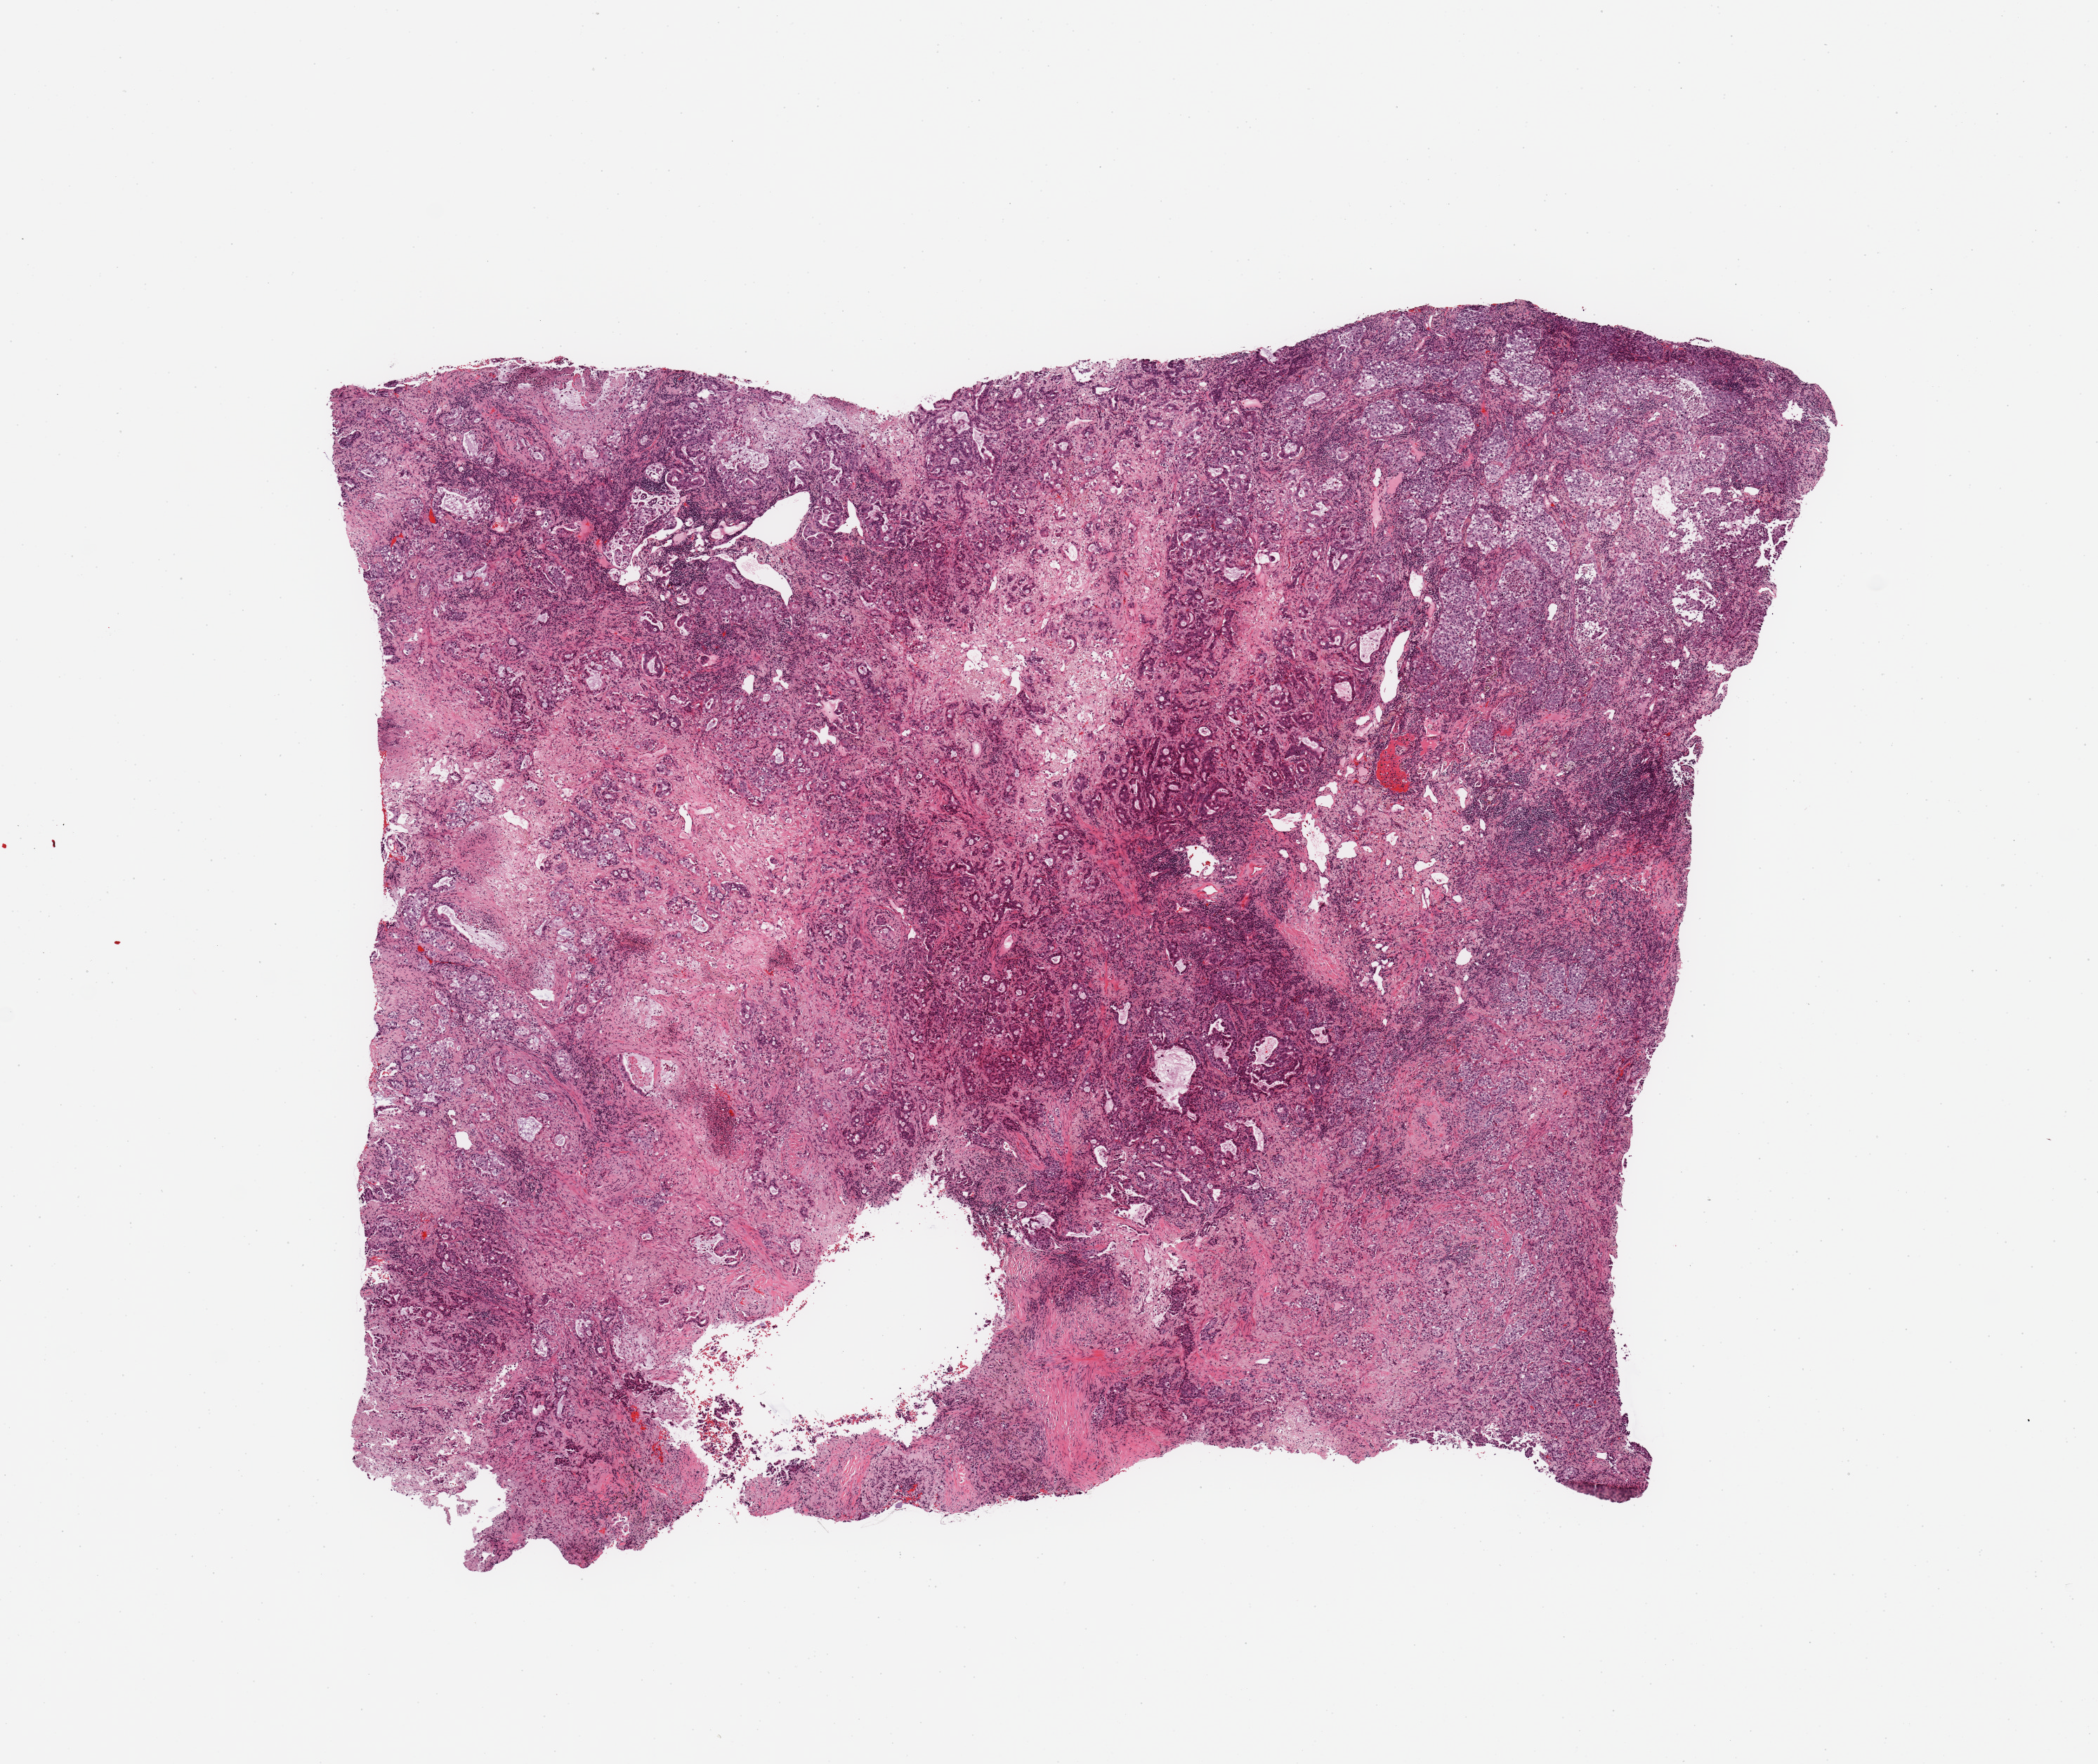
Hematoxylin and eosin (H&E) stained whole-slide image, shown as a low-resolution overview of the whole scanned area (about 11.8 x 9.9 mm, slide scanned at 20x); tumour tissue sample, sampled site: lung. 61-year-old female patient. Composition of this section per pathologist review: tumour nuclei 80%, necrosis 5%.
Histologic diagnosis: Adenocarcinoma, NOS.